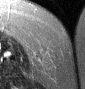
MRI of an extremity soft-tissue mass, one axial slice; position 11 of 46 along the scan axis; T2-weighted fat-saturated; MR volume resampled by the dataset authors to the PET/CT grid (not the native acquisition matrix); 3.27 mm slice thickness; 85 × 89 image matrix, field of view 83 × 87 mm. Female patient. From the clinical record (not read from this slice): histological type: leiomyosarcoma; grade: intermediate; site of the primary tumour: parascapusular.
Outlined on this slice (expert contour drawn on MRI and transferred to this co-registered scan by the dataset authors):
- gross tumour volume including surrounding oedema: bounding box <36,53,57,67> (left, top, right, bottom; pixels)
- gross tumour volume (mass): <43,55,53,65>